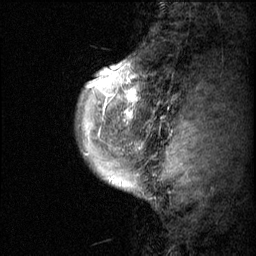
Breast MRI (dynamic contrast-enhanced), one sagittal slice. Position 8 of 60 along the scan axis. Dynamic contrast-enhanced series, image 2 of 3 at this slice position (ordered by acquisition). 1.5 T. TE 4.2 ms, TR 11.1 ms. 2 mm slice thickness. 256 × 256 image matrix, field of view 180 × 180 mm. Patient: female, 50 years.
Outlined on this slice (semi-automatically segmented with operator editing):
- analysis volume of interest (the breast-tissue region the enhancement analysis was run in; not a lesion): bounding box (x1, y1, x2, y2) in pixels: (82, 58, 156, 143)
- tumour enhancement mask (voxels above the 70 % enhancement threshold inside the analysis volume of interest): (85, 60, 141, 143)